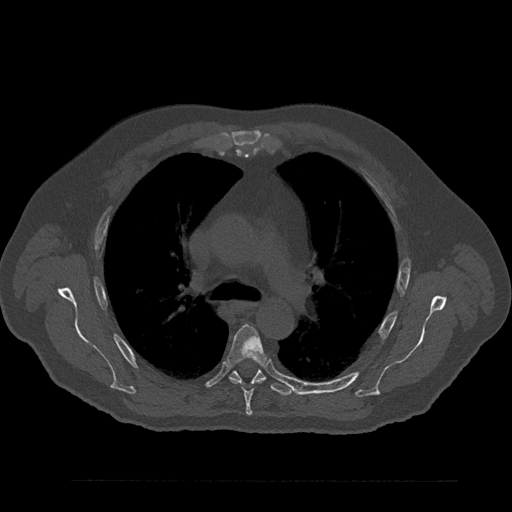
CT including the spine, one axial slice. Position 585 of 797 along the scan axis. 120 kVp. Bone window (W 1800 / L 400 HU). 0.5 mm slice thickness. 512 × 512 image matrix, field of view 430 × 430 mm. Patient: male, 61 years. From the clinical record (not read from this slice): primary cancer: prostate.
Annotated regions visible in this slice (semi-automatic segmentation, software-assisted and operator-edited):
- T5 vertebra: bounding box [x1, y1, x2, y2] px = [227, 325, 266, 416]
- T6 vertebra: [230, 363, 293, 396]